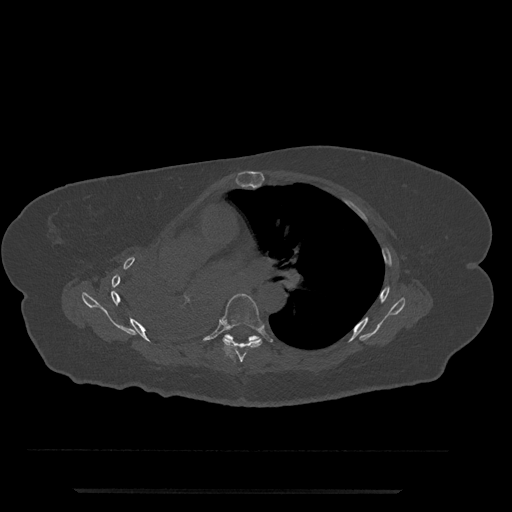
CT including the spine, one axial slice; position 482 of 797 along the scan axis; 120 kVp; bone window (W 1800 / L 400 HU); 0.5 mm slice thickness; 512 × 512 image matrix, field of view 440 × 440 mm. Patient: female, 51 years. From the clinical record (not read from this slice): primary cancer: neuro; vertebrae with lytic lesions (as recorded): T8.
Outlined on this slice (semi-automatically segmented with operator editing):
- T6 vertebra: bounding box (x1, y1, x2, y2) in pixels: (220, 294, 264, 363)
- T7 vertebra: (225, 334, 260, 341)